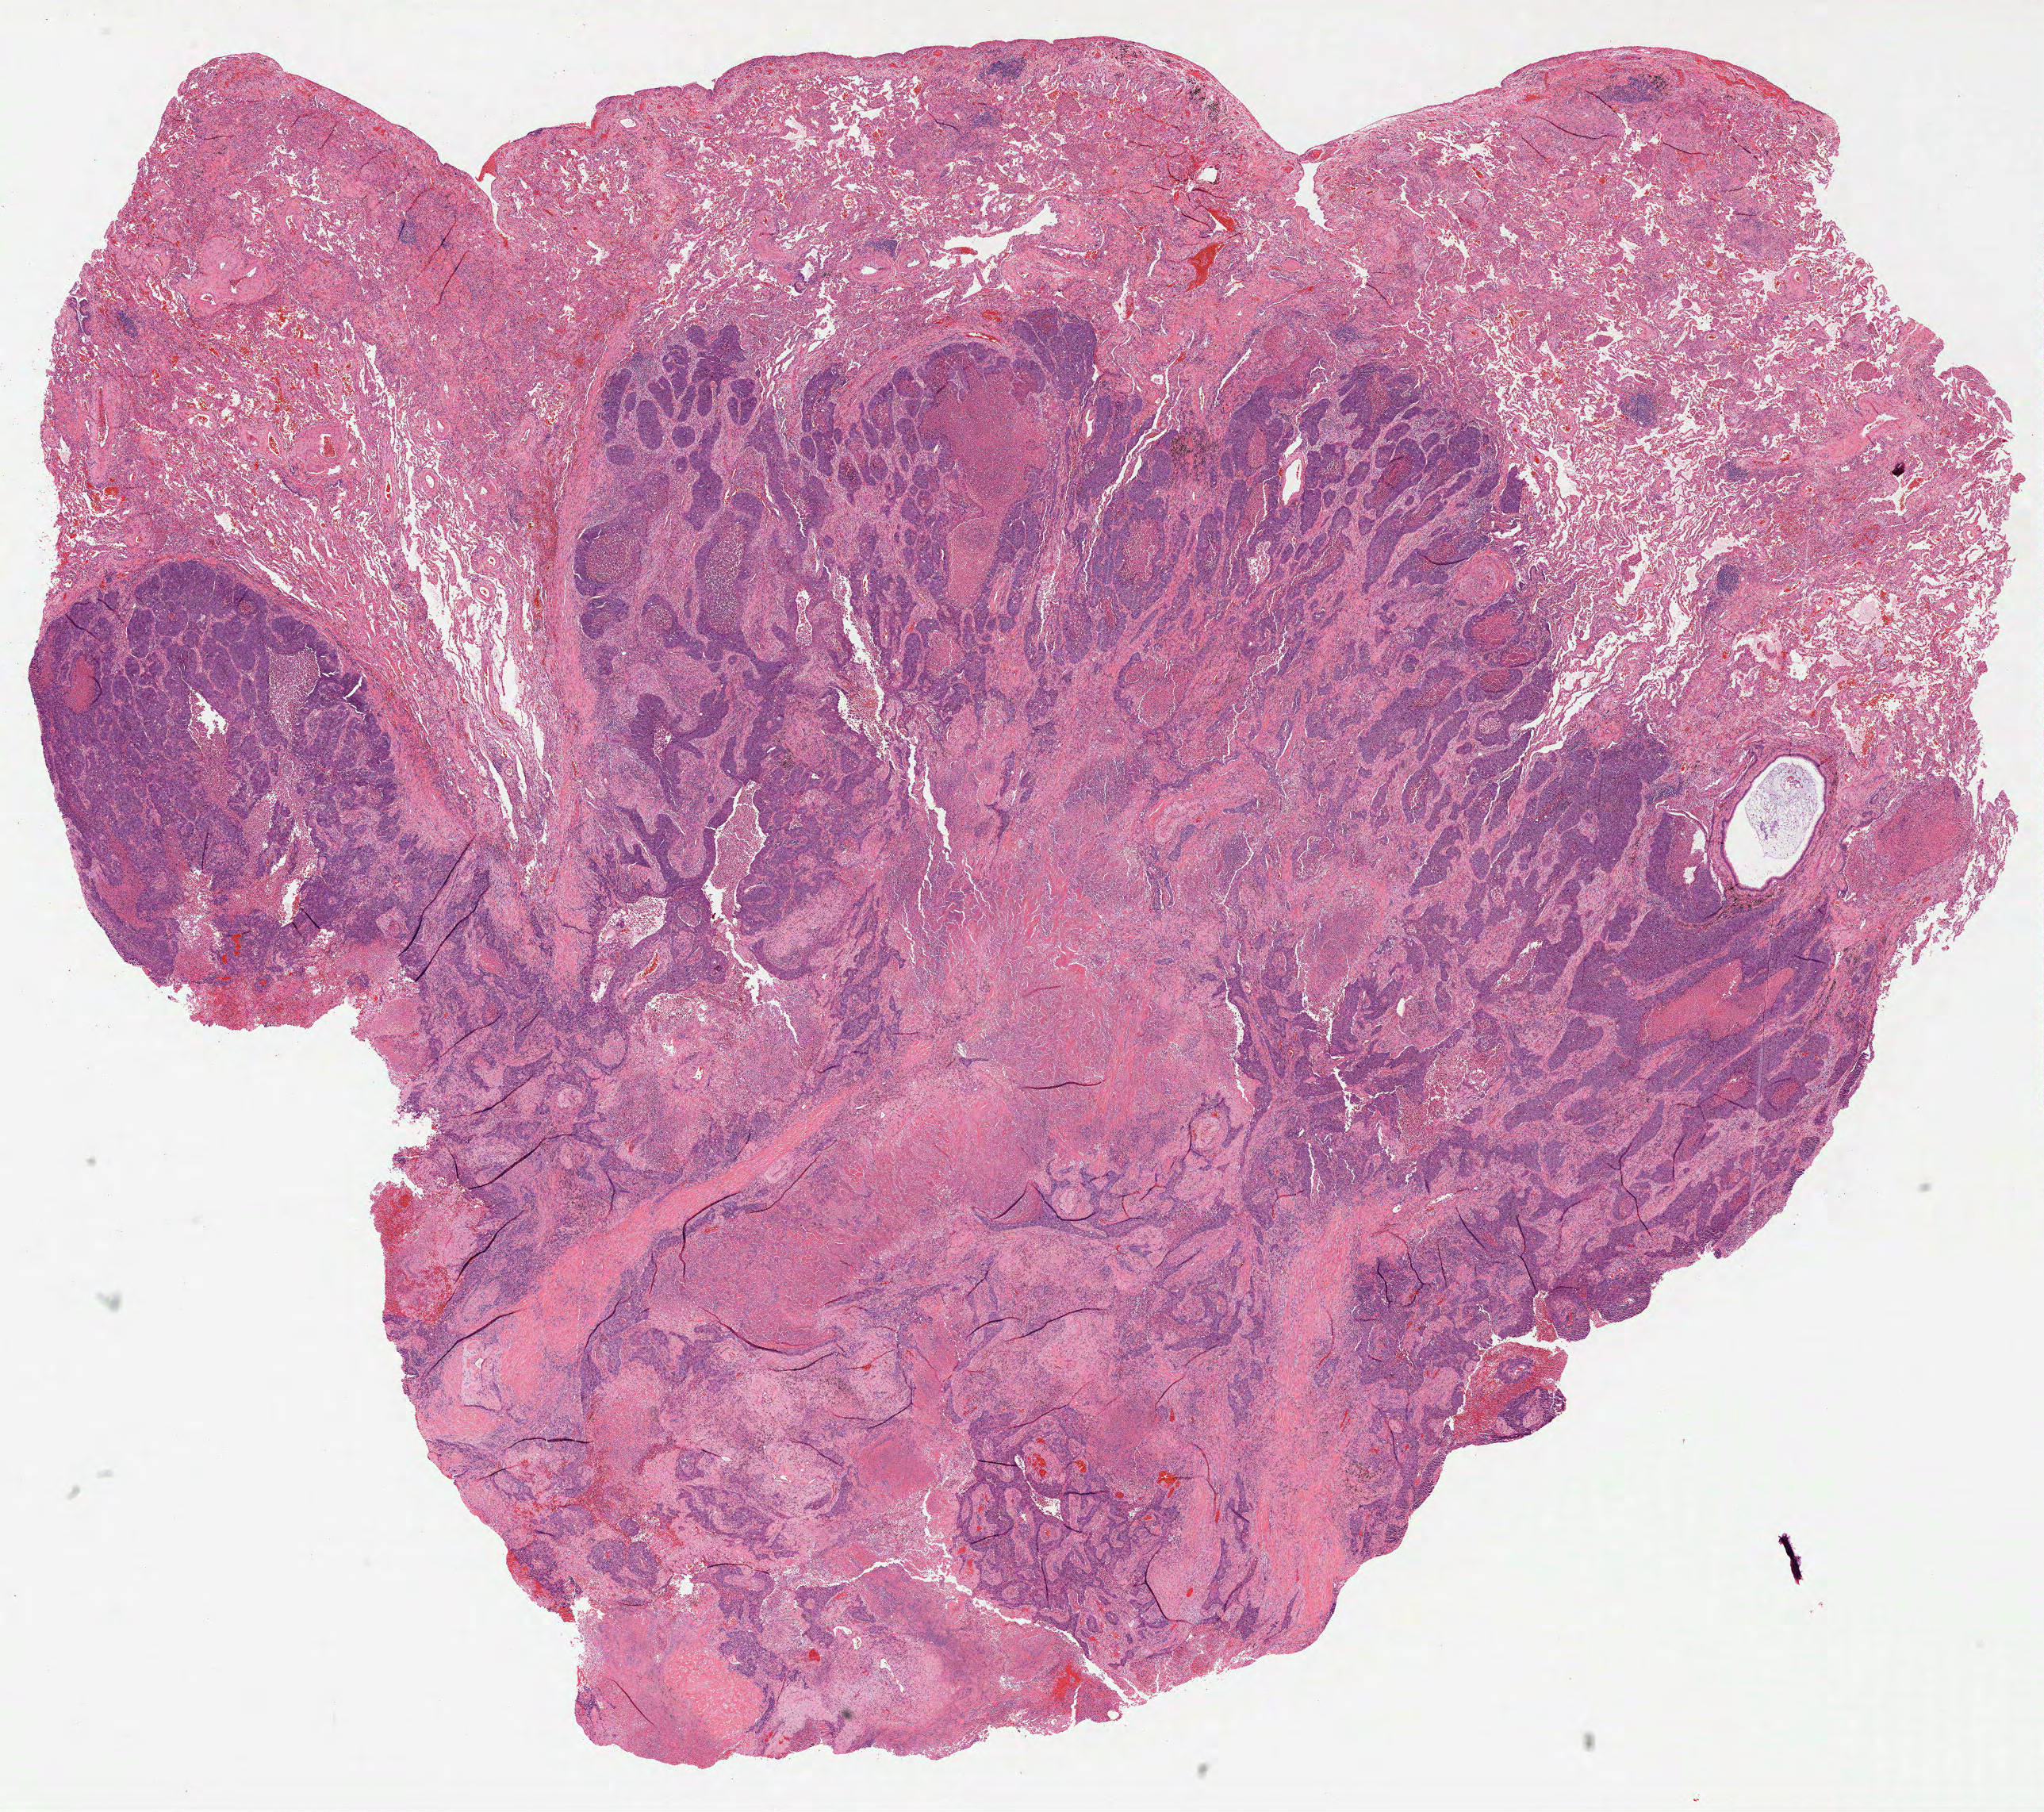
Whole-slide histology image, H&E-stained — a low-resolution overview of the entire scanned area, about 20.8 x 18.4 mm (from a 40x scan); formalin-fixed paraffin-embedded (FFPE) diagnostic section; primary tumour sample from the lung. Male, age 78 years at initial diagnosis.
- AJCC pathologic stage: IB (7th edition)
- pathologic diagnosis: Squamous cell carcinoma, NOS (upper lobe, lung)
- laterality: left